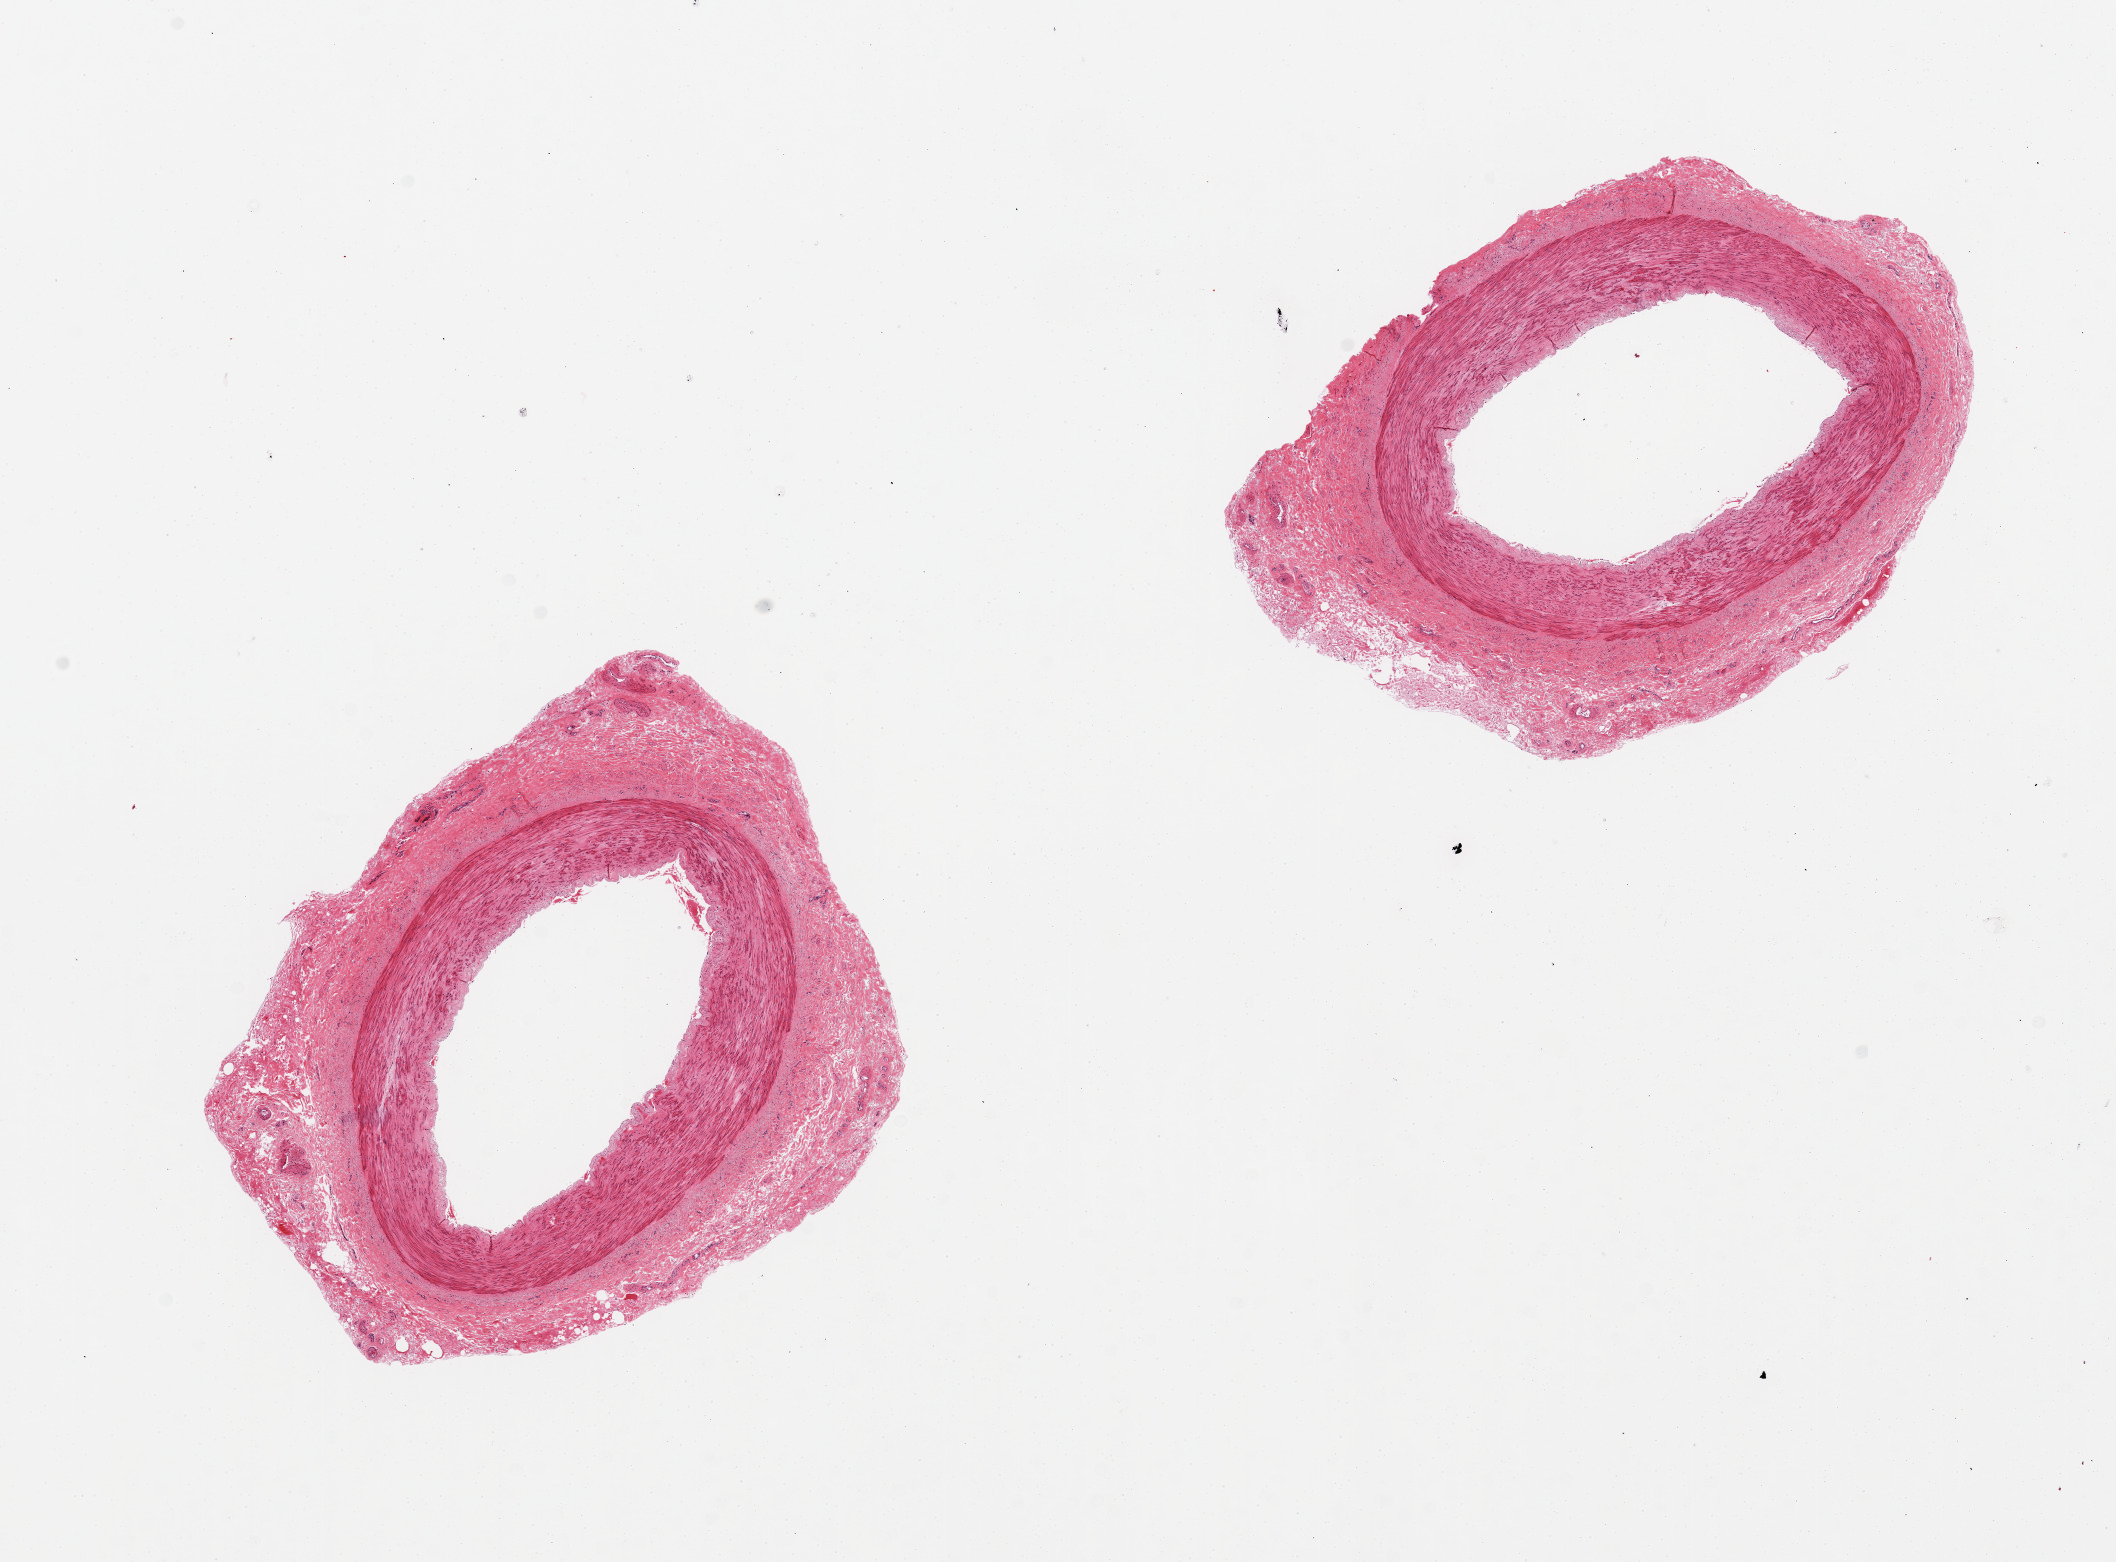
Haematoxylin and eosin whole-slide image — low-resolution overview of the scanned area, about 16.7 x 12.4 mm (from a 20x scan). PAXgene-fixed paraffin-embedded (PFPE) section. Section of tibial artery (target tissue). Tissue donor sample.
Reviewer comment on this tissue sample: 2 pieces, no lesions.